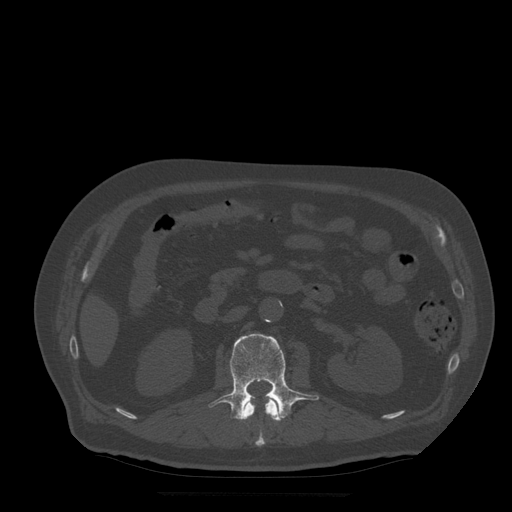
CT including the spine, one axial slice. Slice 174 of 522 in the series (ordered by position). Bone window (W 1800 / L 400 HU). 1.25 mm slice thickness. 512 × 512 image matrix, field of view 420 × 420 mm. Patient age 72 years. From the clinical record (not read from this slice): primary cancer: prostate.
Structures marked on this image (semi-automatic segmentation, software-assisted and operator-edited):
- L1 vertebra: bounding box (x1, y1, x2, y2) in pixels: (242, 396, 281, 447)
- L2 vertebra: (209, 334, 320, 421)